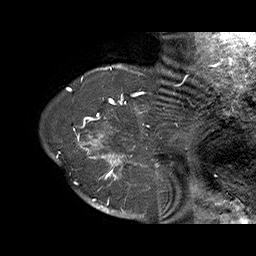
Breast MRI (dynamic contrast-enhanced), one sagittal slice. Position 59 of 70 along the scan axis. Dynamic contrast-enhanced series, time point 2 of 6 at this slice position (early post-contrast). 1.5 T. TE 4.5 ms, TR 32.4 ms. 3 mm slice thickness. 256 × 256 image matrix. Female patient. From the clinical record (not read from this slice): setting: breast cancer imaged before/during neoadjuvant chemotherapy; receptor status: HR-positive, HER2-negative.
Outlined on this slice (semi-automatic segmentation, software-assisted and operator-edited):
- analysis volume of interest (the breast-tissue region the enhancement analysis was run in; not a lesion): bounding box <71,128,159,202> (left, top, right, bottom; pixels)
- tumour enhancement mask (voxels above the 100 % enhancement threshold inside the analysis volume of interest): <73,128,159,202>